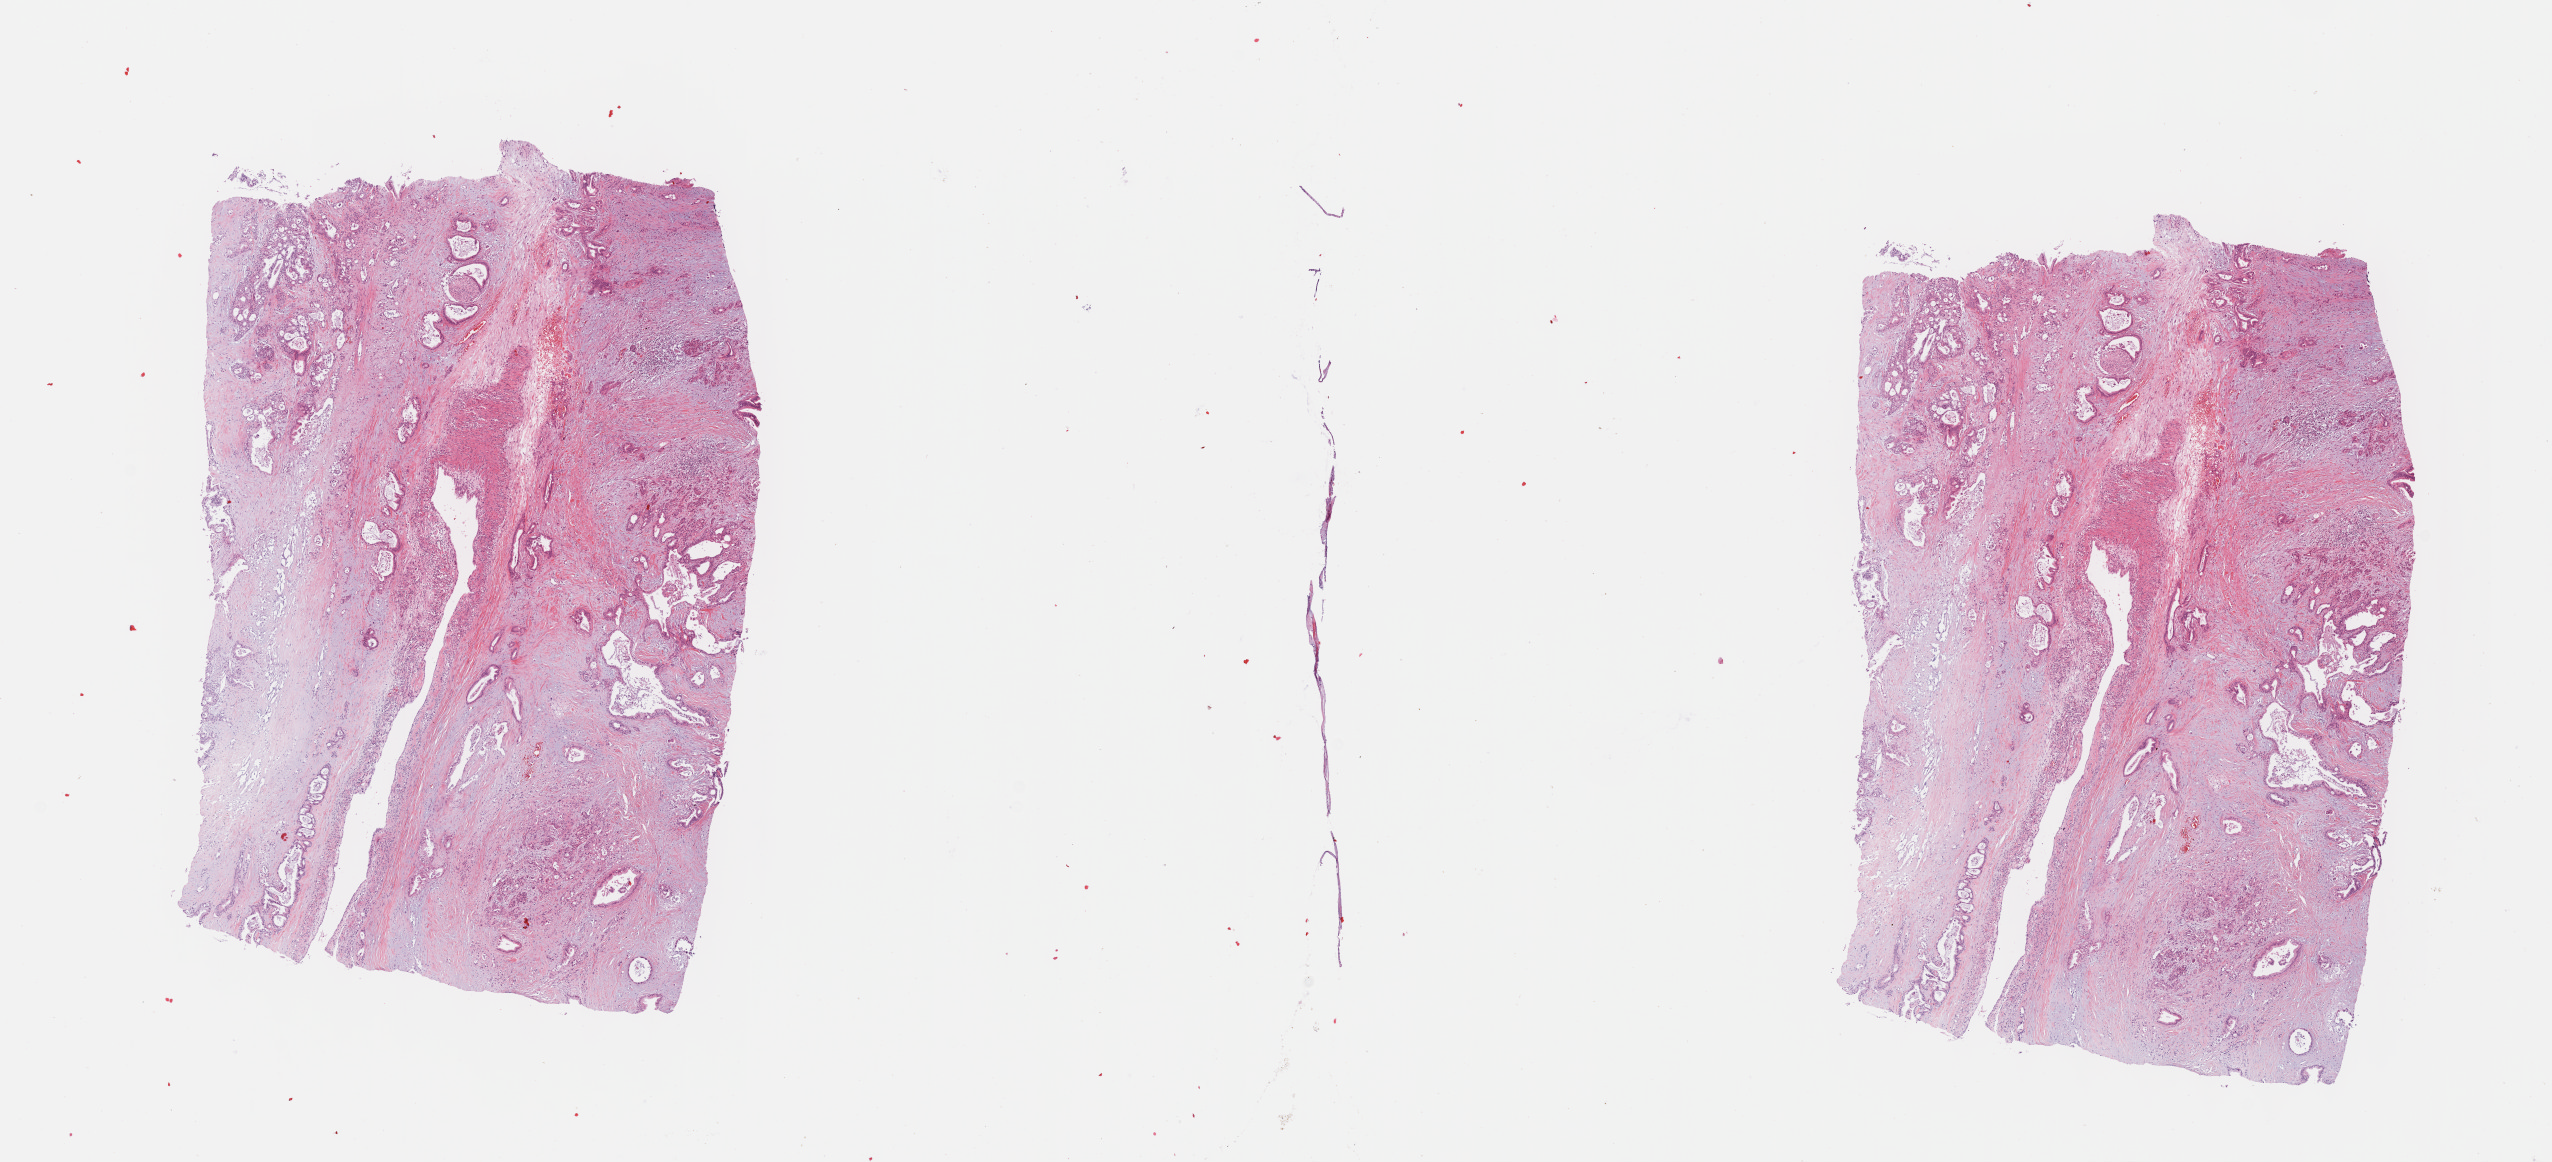
H&E-stained whole-slide image — whole scanned area (about 20.6 x 9.4 mm) shown as a low-resolution overview. Formalin-fixed paraffin-embedded (FFPE) diagnostic section. Primary tumour sample from the pancreas. Male, age 50 years at initial diagnosis. Histologic grade: G2 (moderately differentiated).
* histologic diagnosis: Infiltrating duct carcinoma, NOS (body of pancreas)
* AJCC pathologic stage: IIA